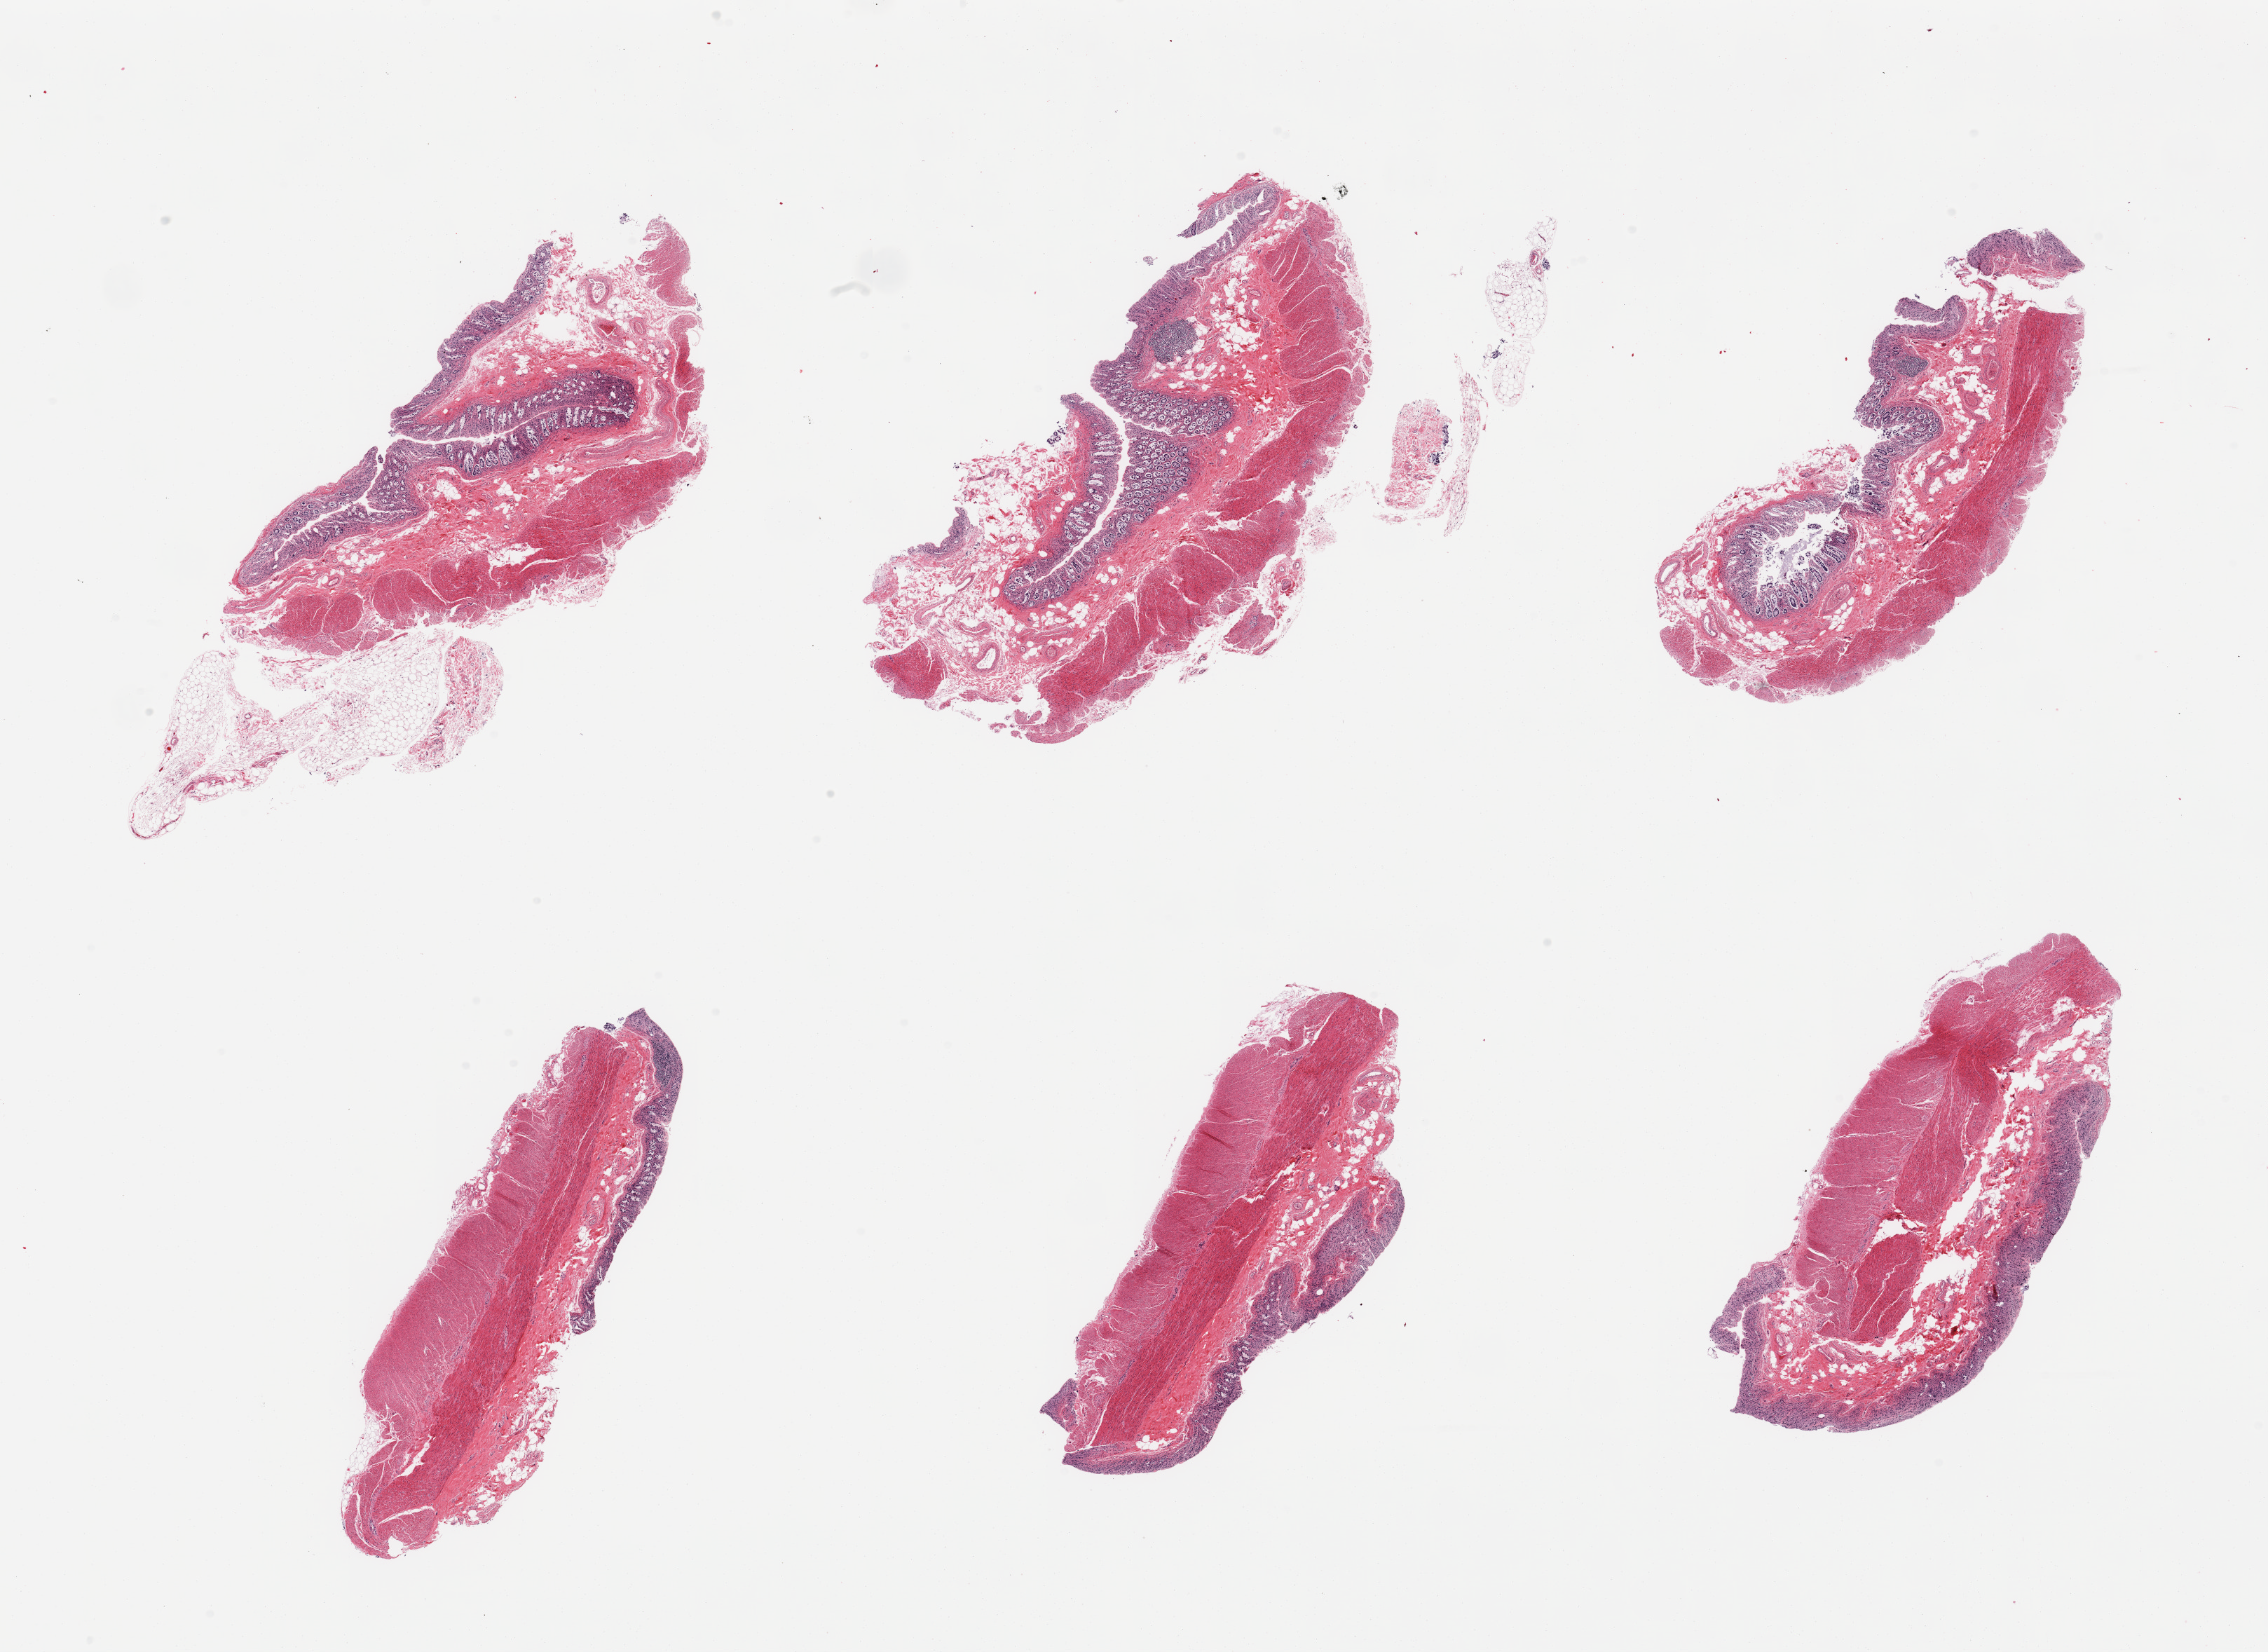
Digitized H&E-stained section — whole scanned area (about 25.6 x 18.6 mm) shown as a low-resolution overview, PAXgene-fixed paraffin-embedded (PFPE) section, sampled site (target tissue): transverse colon, donor tissue sample.
Pathologist's review note for this sample: 6 pieces; mucosal autolysis varies from moderate to severe; muscularis well preserved.